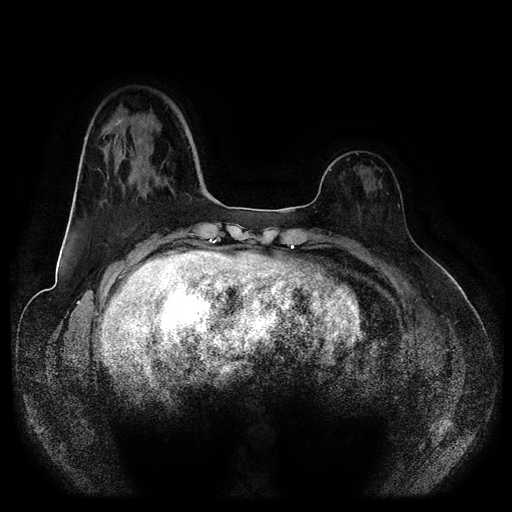
Breast MRI (dynamic contrast-enhanced, multi-phase), one axial slice. Position 30 of 116 along the scan axis. Dynamic contrast-enhanced series, time point 2 of 5 at this slice position (early post-contrast). 1.5 T. TE 2.6 ms, TR 5.2 ms. 2 mm slice thickness. 512 × 512 image matrix, field of view 380 × 380 mm. Female patient, age 50 years.
Outlined on this slice (semi-automatically segmented with operator editing):
- breast lesion (labelled benign in the annotation): box from (x=130, y=137) to (x=144, y=157) px